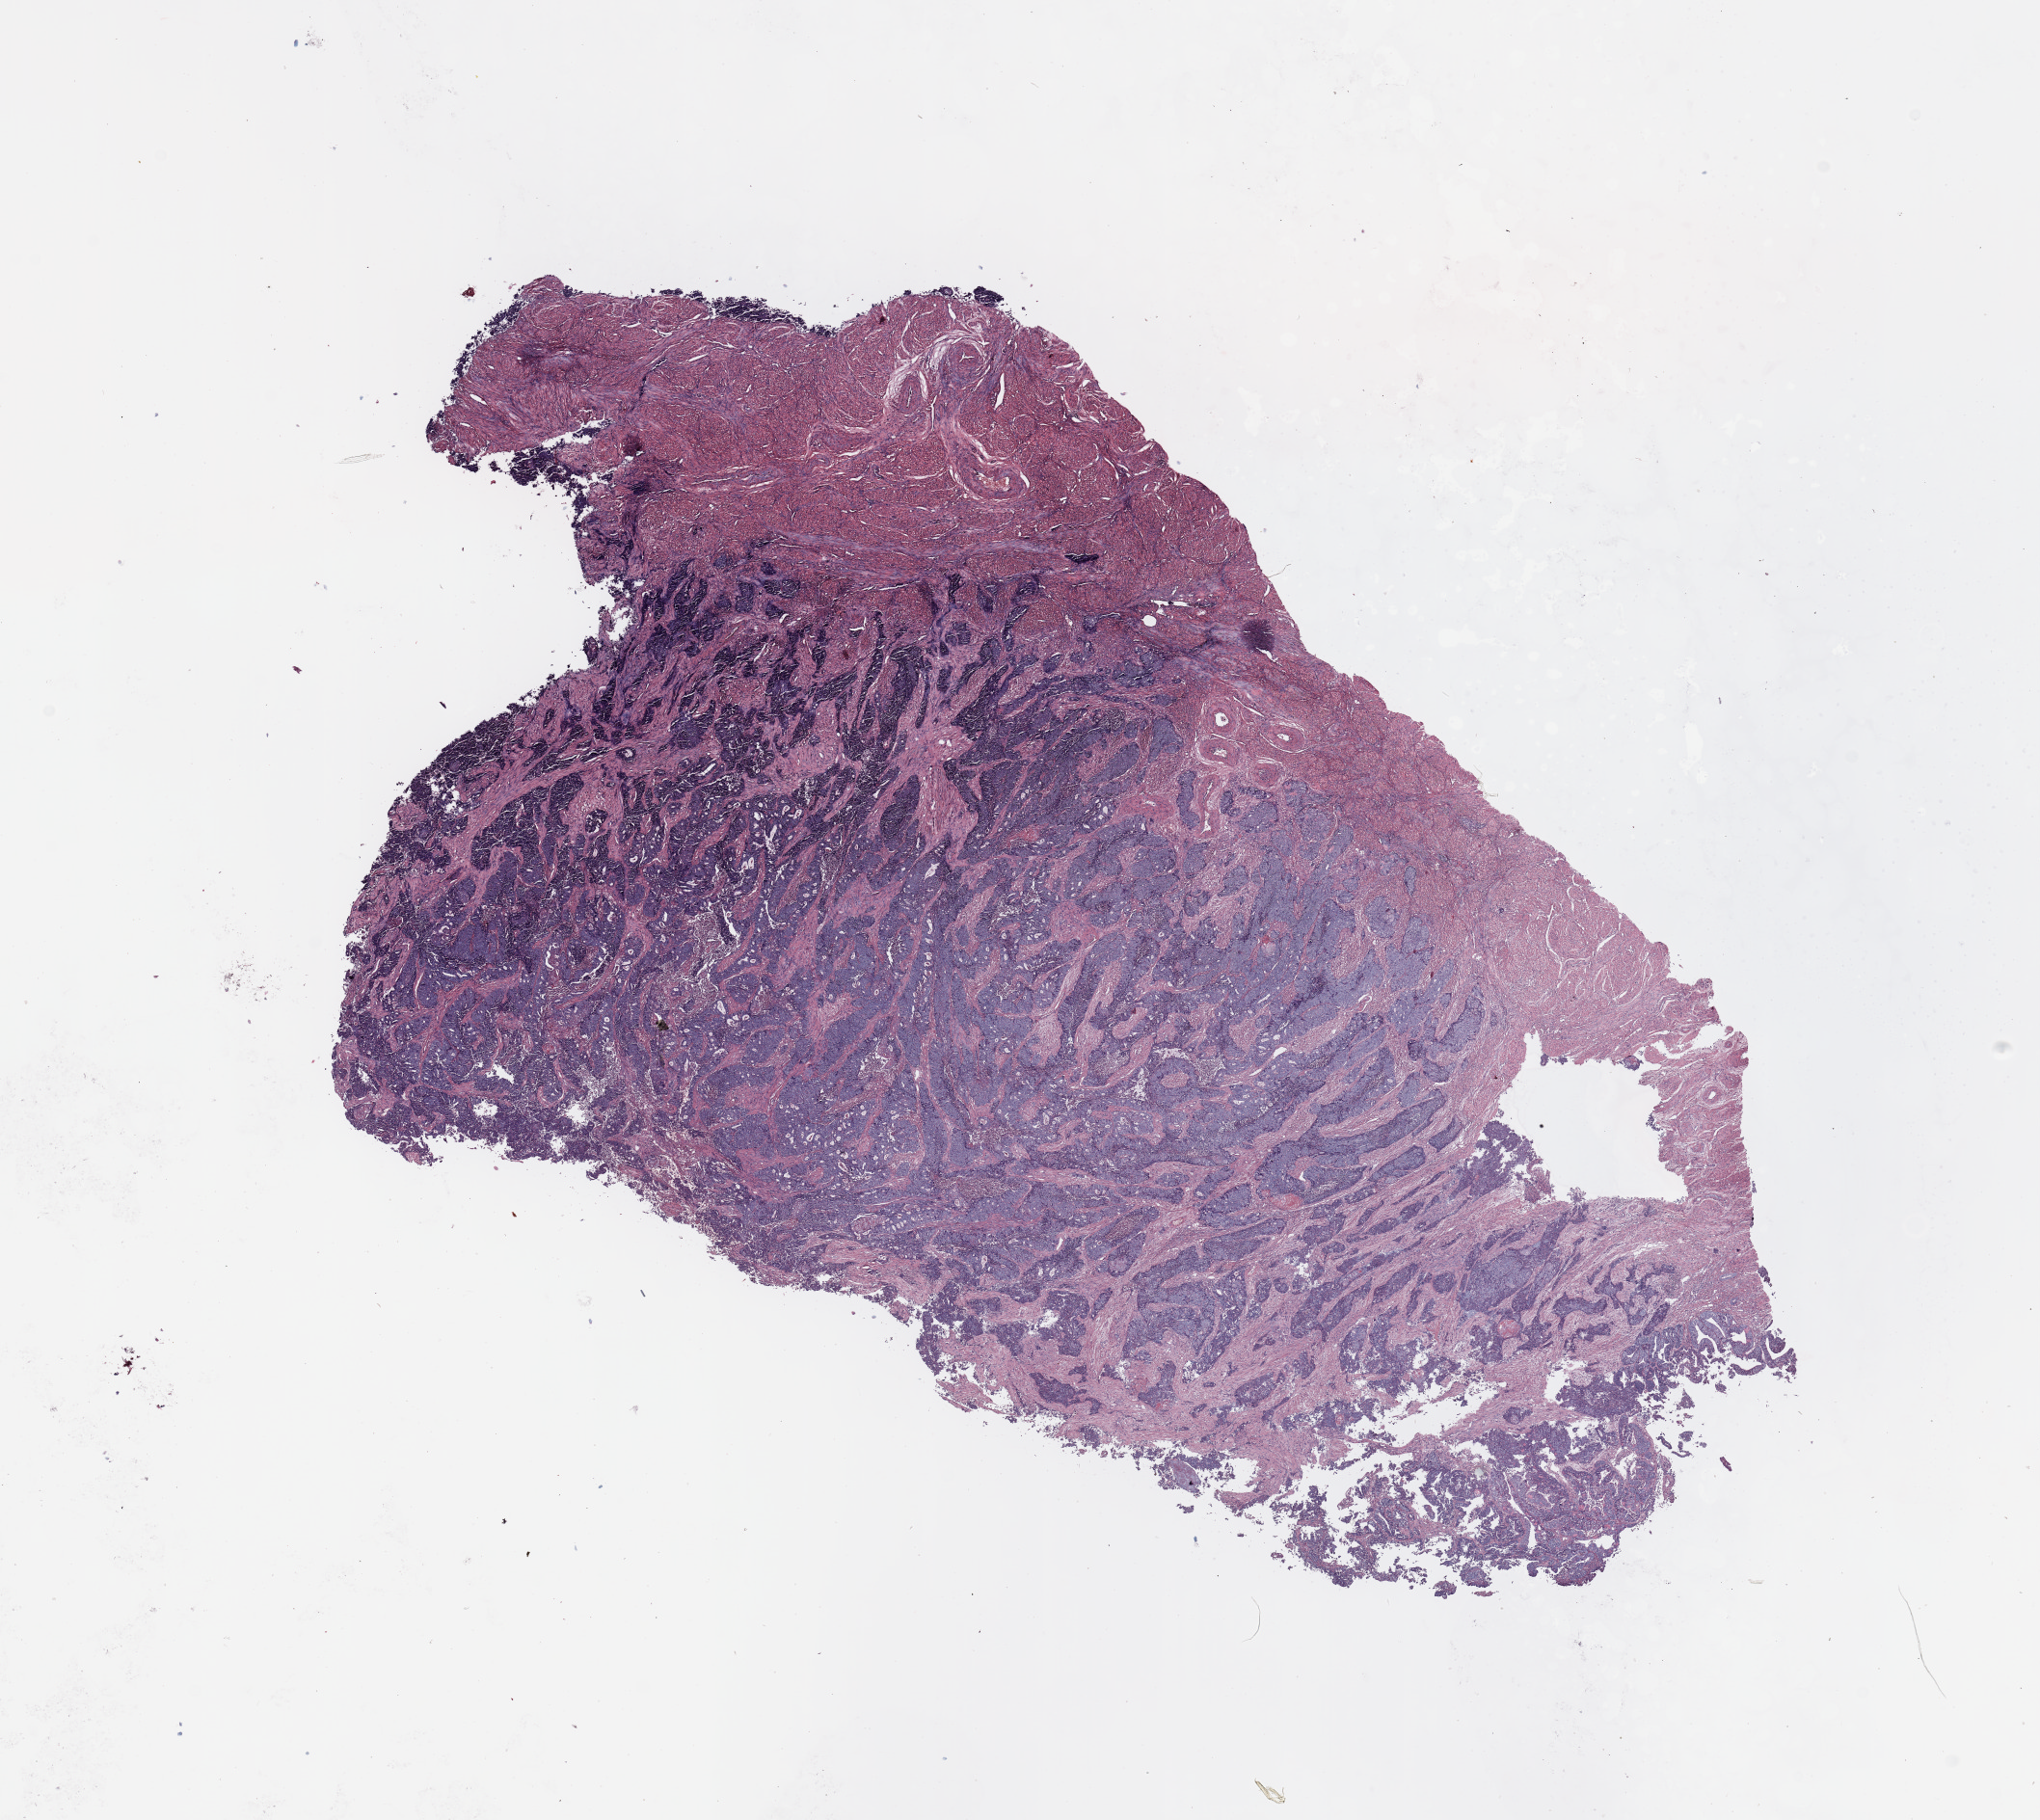
Whole-slide histology image, H&E — shown as a low-resolution overview of the whole scanned area (about 16.7 x 14.9 mm, slide scanned at 20x); tumour tissue sample, uterus. 59-year-old female patient. Histologic grade: G2 (moderately differentiated).
* histologic diagnosis: Endometrioid adenocarcinoma, NOS
* AJCC pathologic stage: II